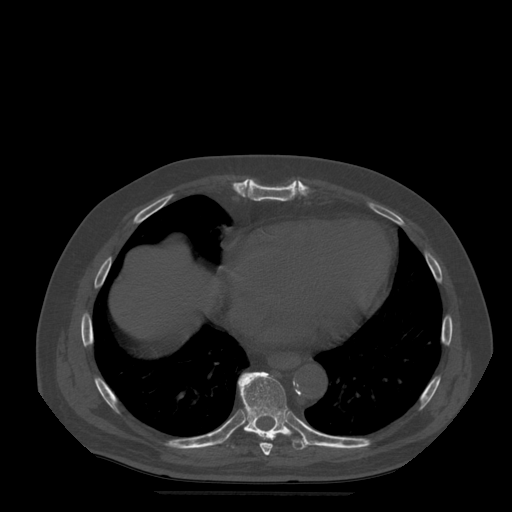
CT including the spine, one axial slice; position 298 of 522 along the scan axis; bone window (W 1800 / L 400 HU); 1.25 mm slice thickness; 512 × 512 image matrix, field of view 420 × 420 mm. Patient age 72 years. Case-level facts recorded for this patient, not image findings: primary cancer: prostate.
Structures marked on this image (semi-automatic segmentation, software-assisted and operator-edited):
- T8 vertebra: bounding box <252,432,273,456> (left, top, right, bottom; pixels)
- T9 vertebra: <229,372,308,450>